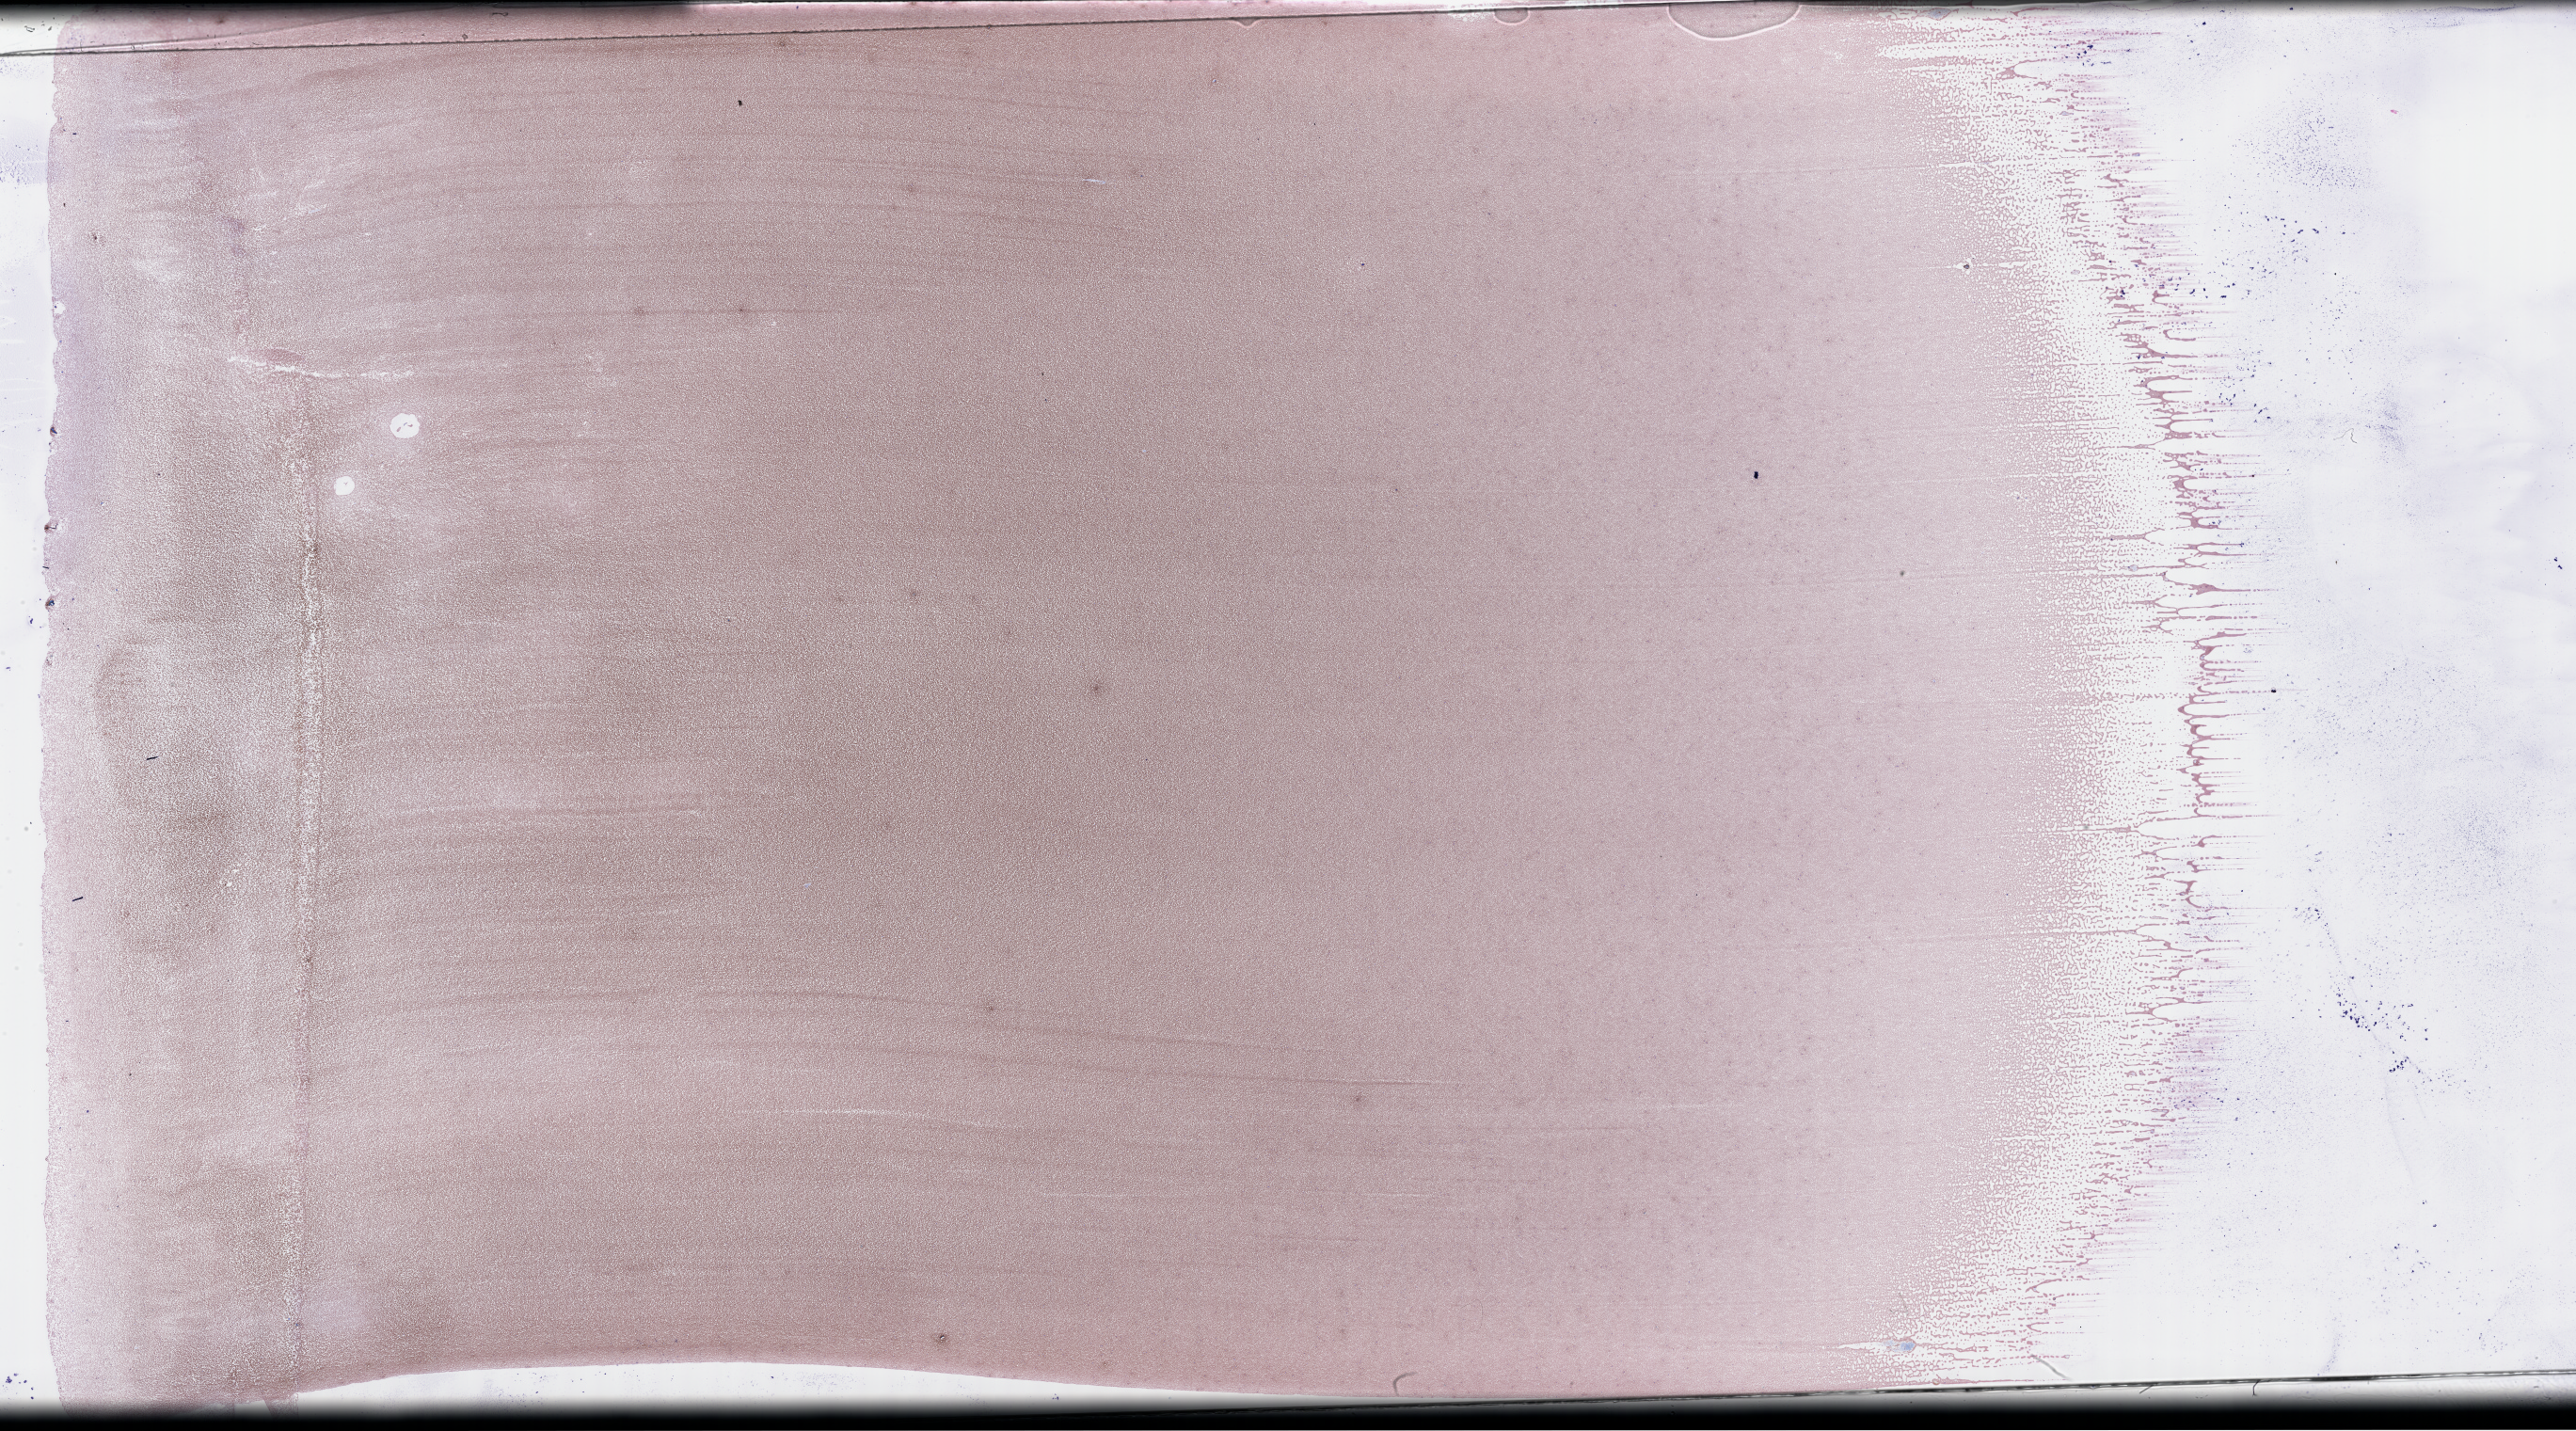
Wright–Giemsa-stained whole blood smear, whole-slide image, low-resolution overview of the scanned area, about 44.2 x 24.6 mm; smear from an EDTA sample; collected on treatment. Patient: female.
From a patient with: Plasma Cell Myeloma.